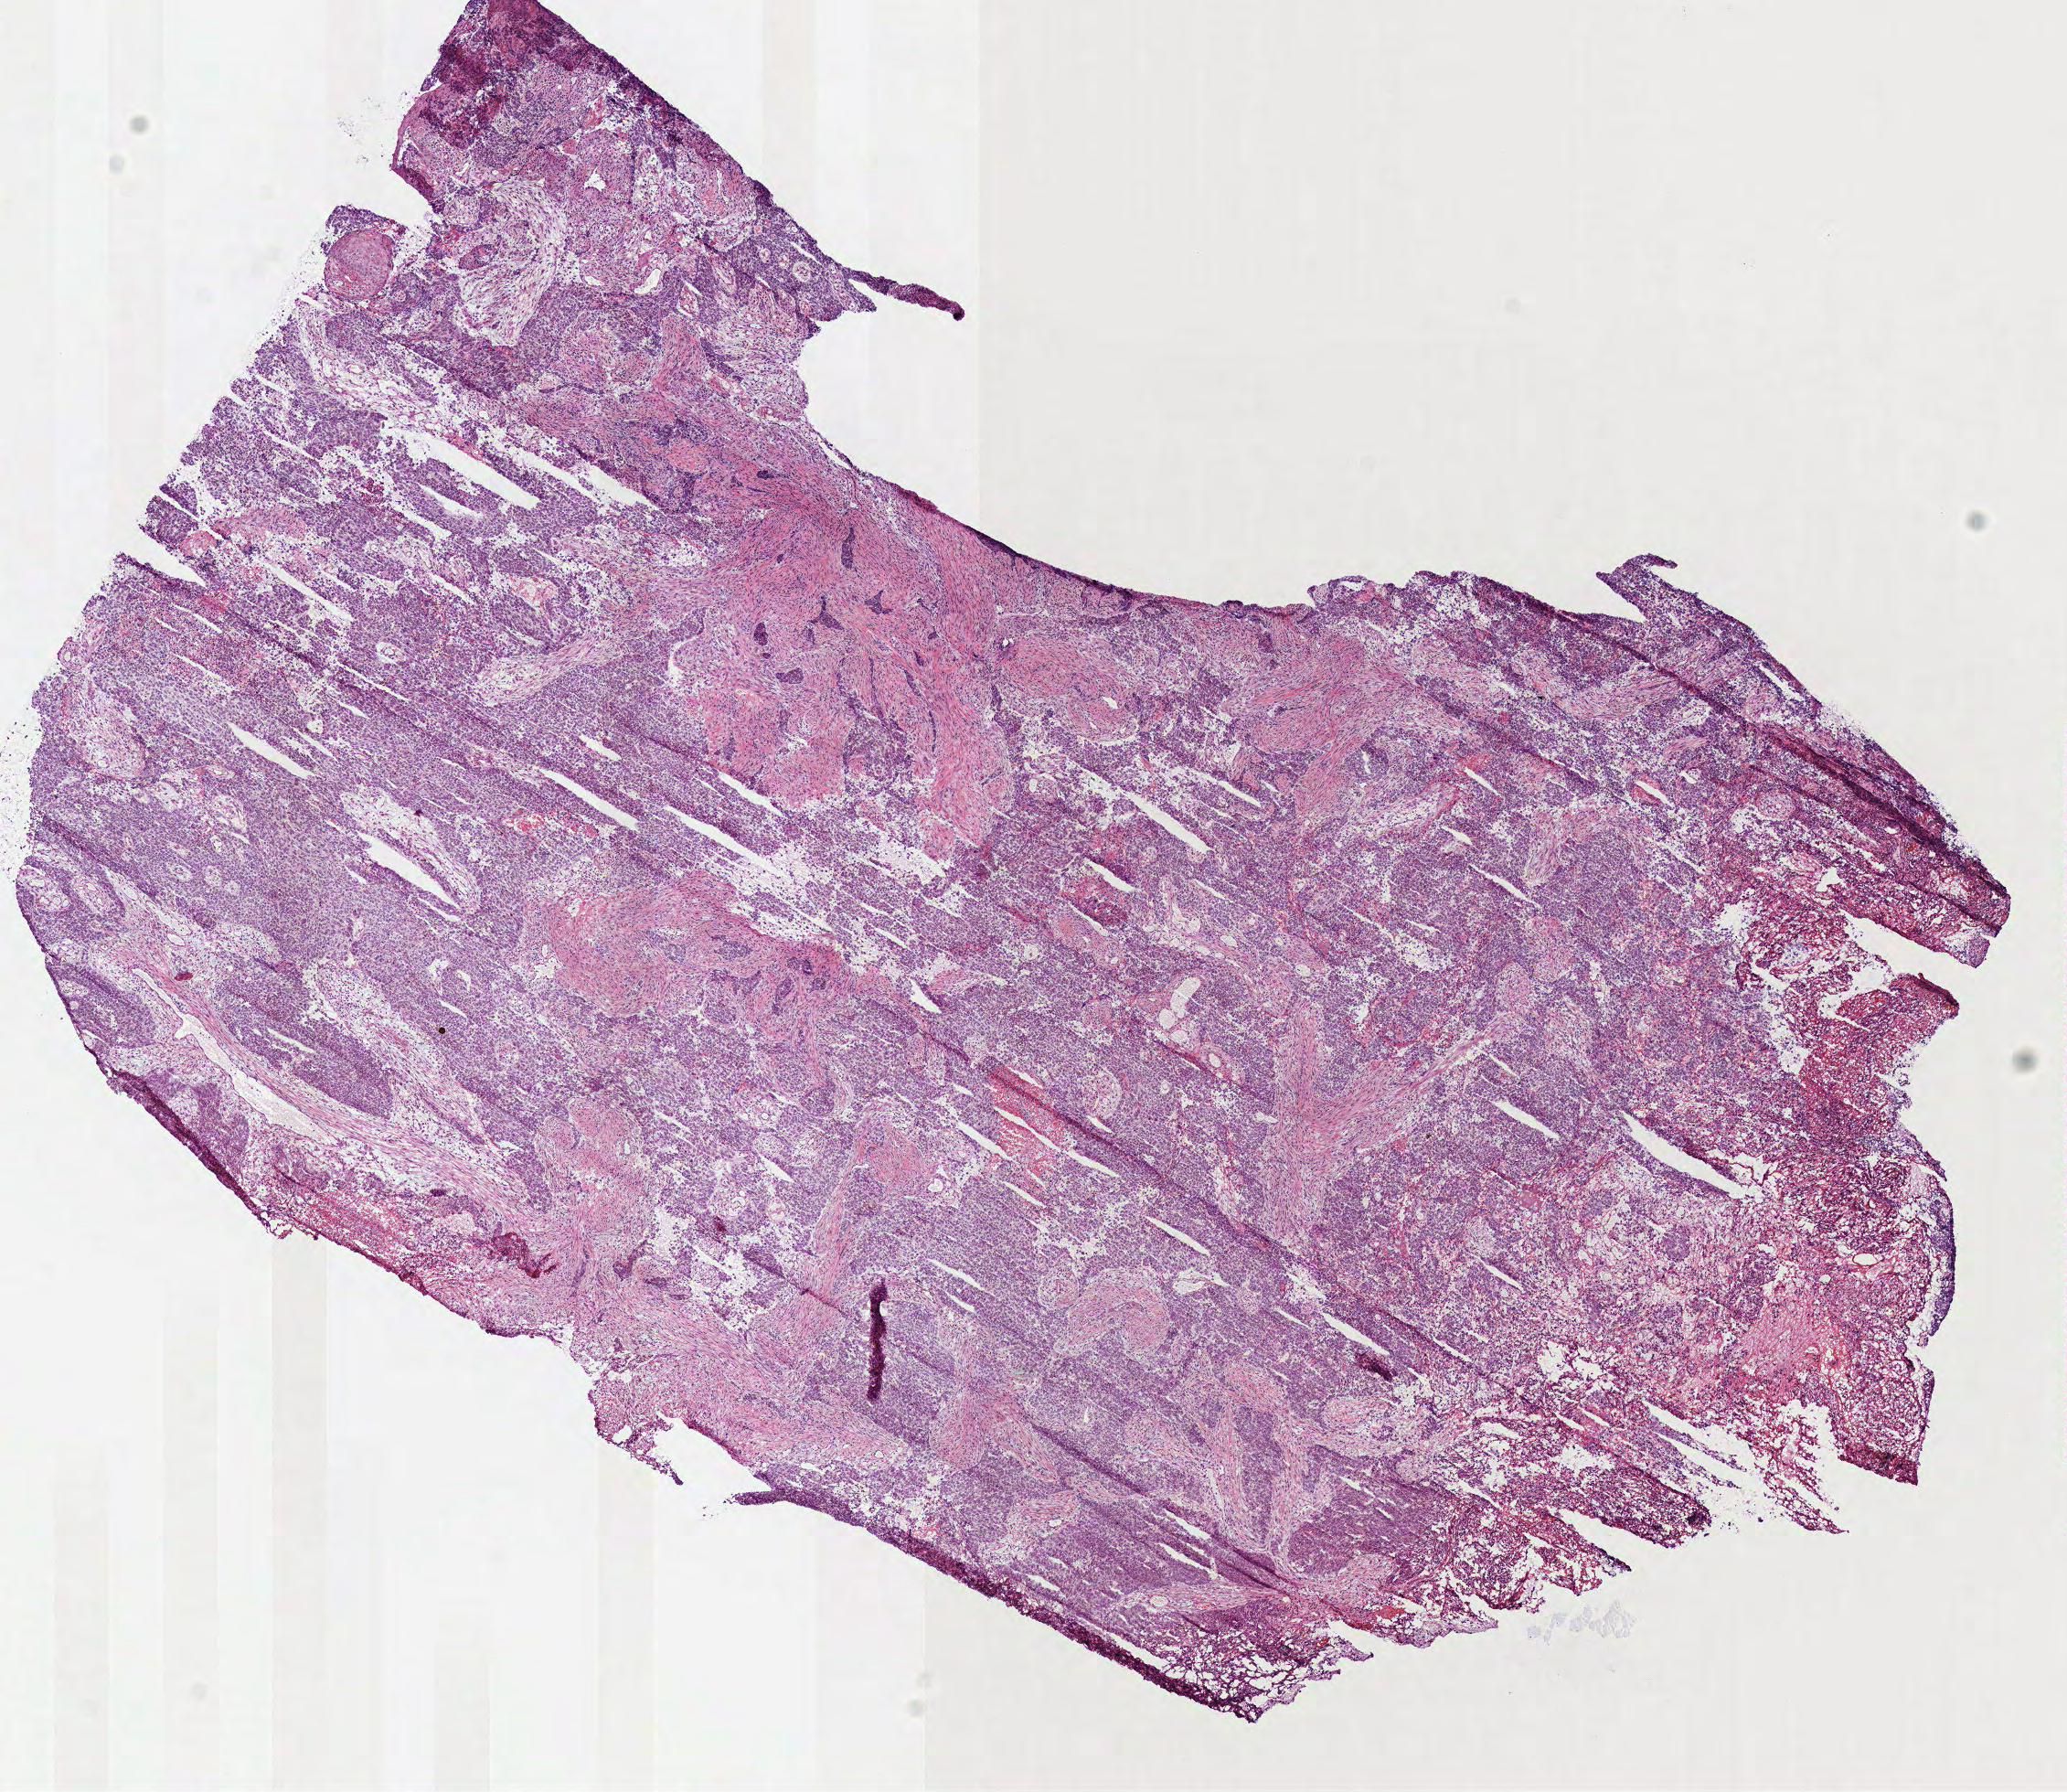
Whole-slide histology image, H&E-stained — a low-resolution overview of the entire scanned area, about 8.9 x 7.7 mm, frozen section from the bottom of the tissue portion, head and neck, primary tumour sample. Patient: male, age at initial diagnosis 75 years.
Pathologic diagnosis: Squamous cell carcinoma, NOS (base of tongue, NOS).